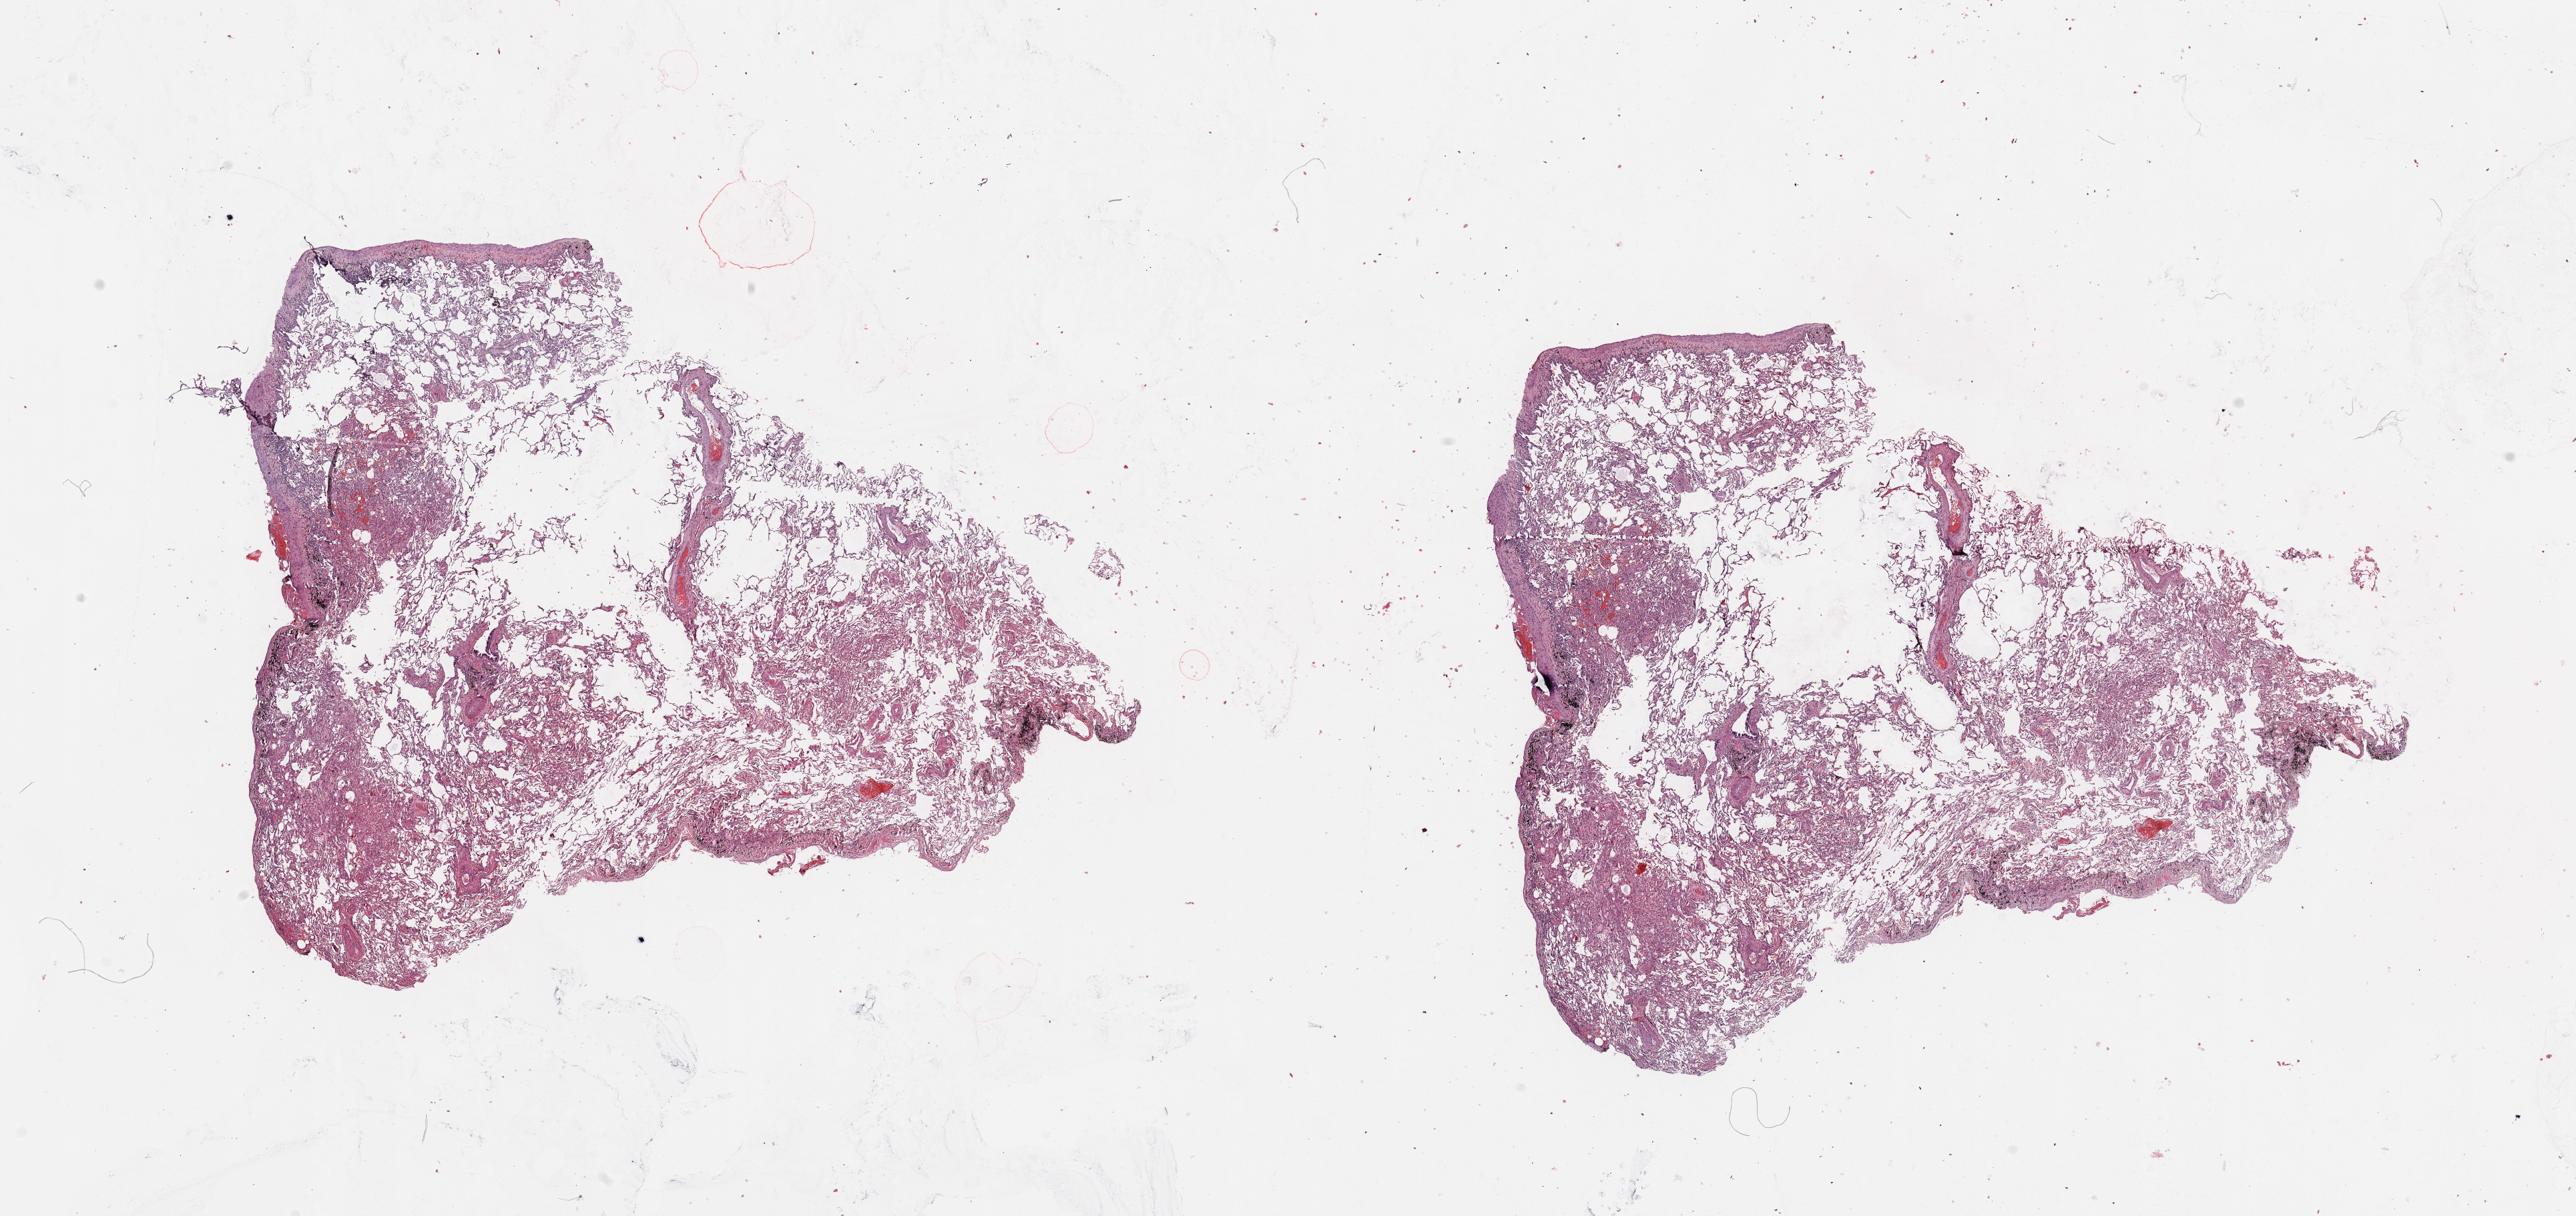
Hematoxylin and eosin (H&E) stained whole-slide image — whole scanned area (about 30.5 x 14.4 mm) shown as a low-resolution overview; normal (non-tumour) tissue sample, lung. Male, 59 y/o.
This section: normal (non-tumour) tissue from the same patient. Patient diagnosis: Adenocarcinoma, NOS.